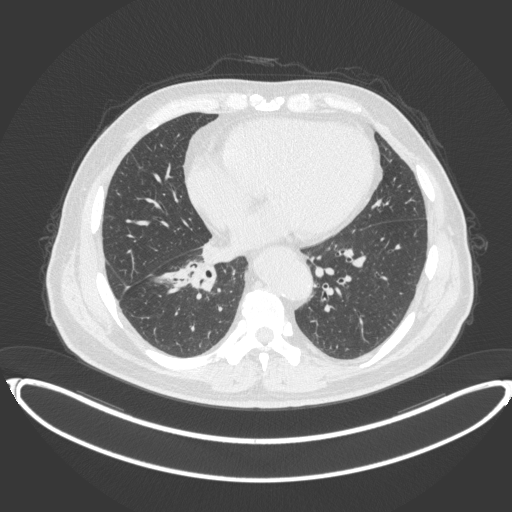
Chest CT, one axial slice. Reconstruction kernel B31f. Lung window (W 1500 / L -600 HU). 512 × 512 image matrix, field of view 448 × 448 mm. Male patient, age 61 years. Case-level facts recorded for this patient, not image findings: clinical TNM (as recorded): T1b N1 M0.
Structures marked on this image (rectangle marked by the reading radiologist):
- lung tumour (recorded histology: squamous cell carcinoma): box from (x=179, y=253) to (x=219, y=291) px